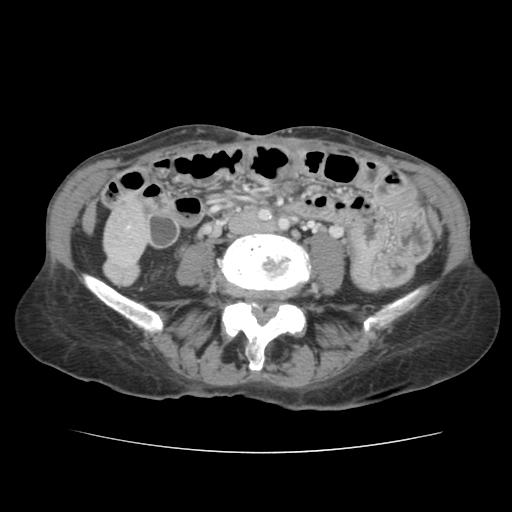
Contrast-enhanced abdominal CT, one axial slice. Slice 16 of 136 in the series (ordered by position). Soft-tissue window (W 400 / L 40 HU). 2.5 mm slice thickness. 512 × 512 image matrix, field of view 319 × 319 mm. Female patient, age 77 years. Case-level facts recorded for this patient, not image findings: diagnosis: colorectal cancer liver metastases, imaged before liver resection.
Outlined on this slice (manually delineated by an expert):
- liver: bounding box (x1, y1, x2, y2) in pixels: (106, 201, 146, 275)